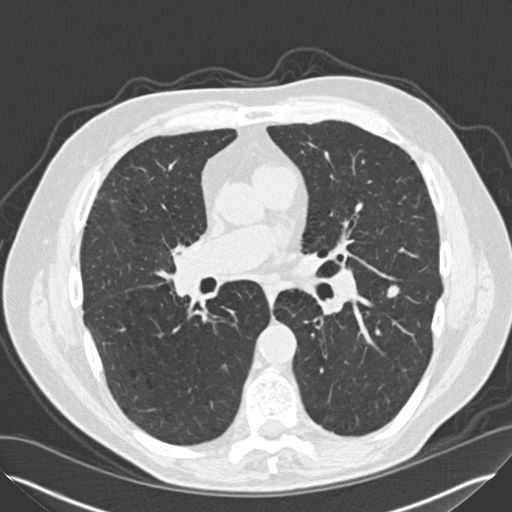
Low-dose screening chest CT, one axial slice; position 75 of 149 along the scan axis; reconstruction kernel B30f; 120 kVp; lung window (W 1500 / L -600 HU); 2 mm slice thickness; 512 × 512 image matrix, field of view 370 × 370 mm.
Structures marked on this image (expert manual segmentation):
- lesion 1 (tumor, lower lobe of left lung): bounding box [x1, y1, x2, y2] px = [387, 285, 400, 298]